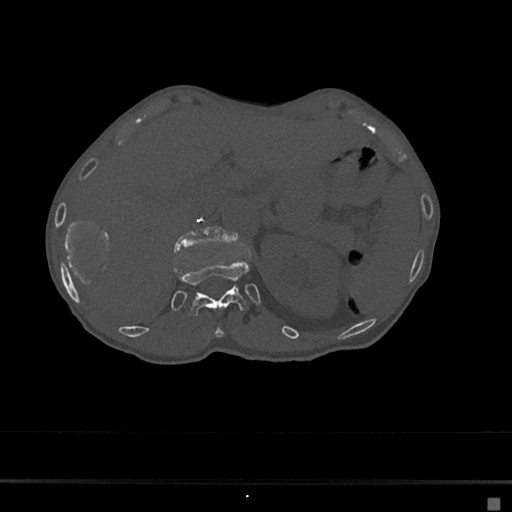
CT including the spine, one axial slice. Position 120 of 797 along the scan axis. Bone window (W 1800 / L 400 HU). 0.5 mm slice thickness. 512 × 512 image matrix, field of view 360 × 360 mm. Patient: female, 68 years. Case-level facts recorded for this patient, not image findings: primary cancer: renal.
Structures marked on this image (semi-automatically segmented with operator editing):
- L1 vertebra: box from (x=174, y=226) to (x=237, y=252) px
- T11 vertebra: (x=215, y=327)–(x=224, y=338)
- T12 vertebra: (x=174, y=258)–(x=250, y=318)